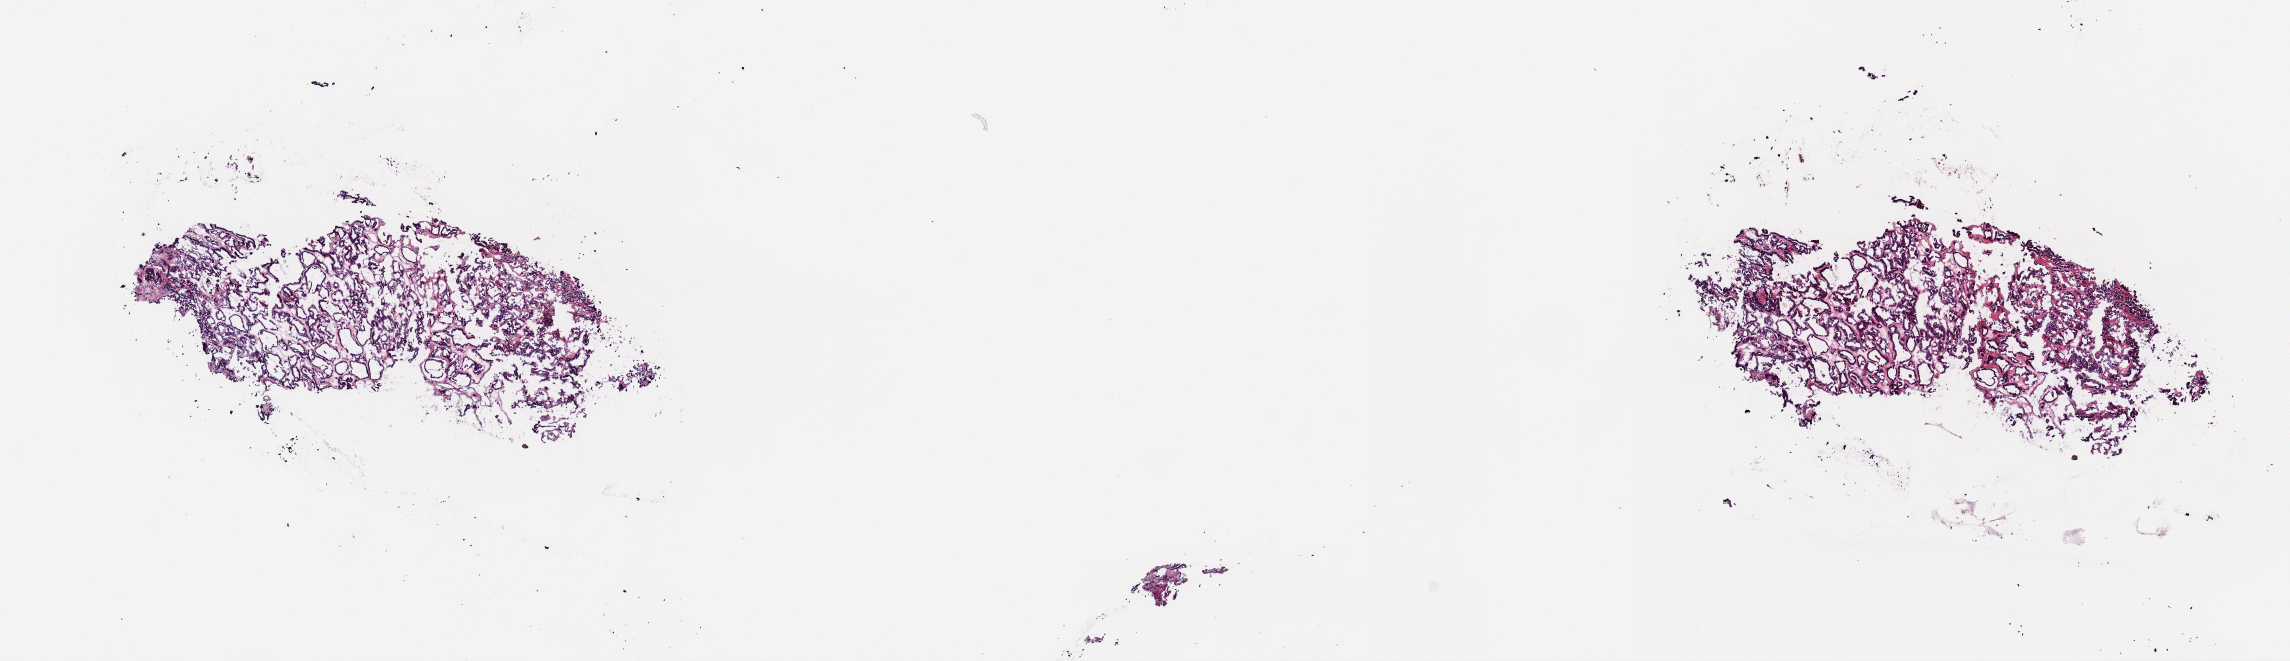
Whole-slide histology image, H&E-stained, shown as a low-resolution overview of the whole scanned area (about 18.1 x 5.2 mm, from a 40x scan), frozen section from the top of the tissue portion, thyroid, primary tumour sample. Female patient; age at initial diagnosis 34 years. Slide review estimates, as recorded: tumour cells 85%, tumour nuclei 85%, normal cells 0%, stromal cells 15%, necrosis 0%. Infiltration values recorded for this section: lymphocyte infiltration 2%, monocyte infiltration 1%, neutrophil infiltration 0%.
Diagnosis: Papillary adenocarcinoma, NOS (thyroid gland). Lymph nodes positive (case pathology): 2 of 3 examined. TNM: T2 N1a MX. AJCC pathologic stage: I (6th edition).